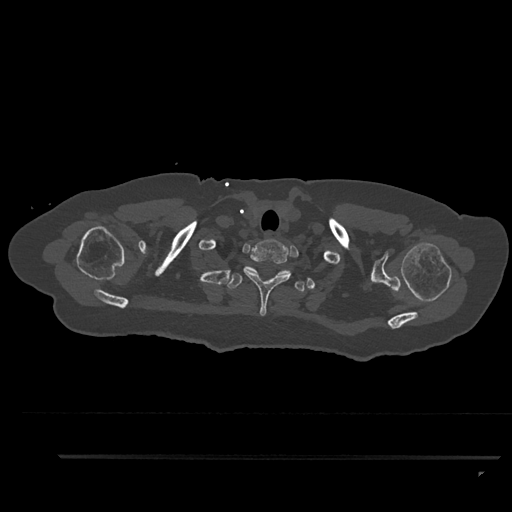
CT including the spine, one axial slice. Position 750 of 797 along the scan axis. 120 kVp. Bone window (W 1800 / L 400 HU). 0.5 mm slice thickness. 512 × 512 image matrix. Female patient, age 44 years. Case-level facts recorded for this patient, not image findings: primary cancer: renal; vertebrae with lytic lesions (as recorded): L1.
Outlined on this slice (semi-automatically segmented with operator editing):
- T1 vertebra: box from (x=241, y=239) to (x=291, y=316) px
- T2 vertebra: (x=227, y=273)–(x=305, y=292)